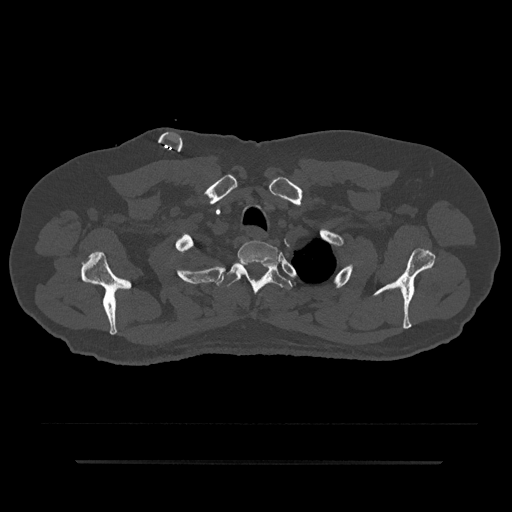
CT including the spine, one axial slice. Slice 712 of 797 in the series (ordered by position). Reconstruction kernel Br40s/3. 120 kVp. Bone window (W 1800 / L 400 HU). 512 × 512 image matrix, field of view 464 × 464 mm. Male patient, age 59 years. Case-level facts recorded for this patient, not image findings: primary cancer: bile ducts; vertebrae with lytic lesions (as recorded): T10.
Annotated regions visible in this slice (semi-automatic segmentation, software-assisted and operator-edited):
- T1 vertebra: bounding box [x1, y1, x2, y2] px = [236, 241, 278, 264]
- T2 vertebra: [216, 262, 292, 295]